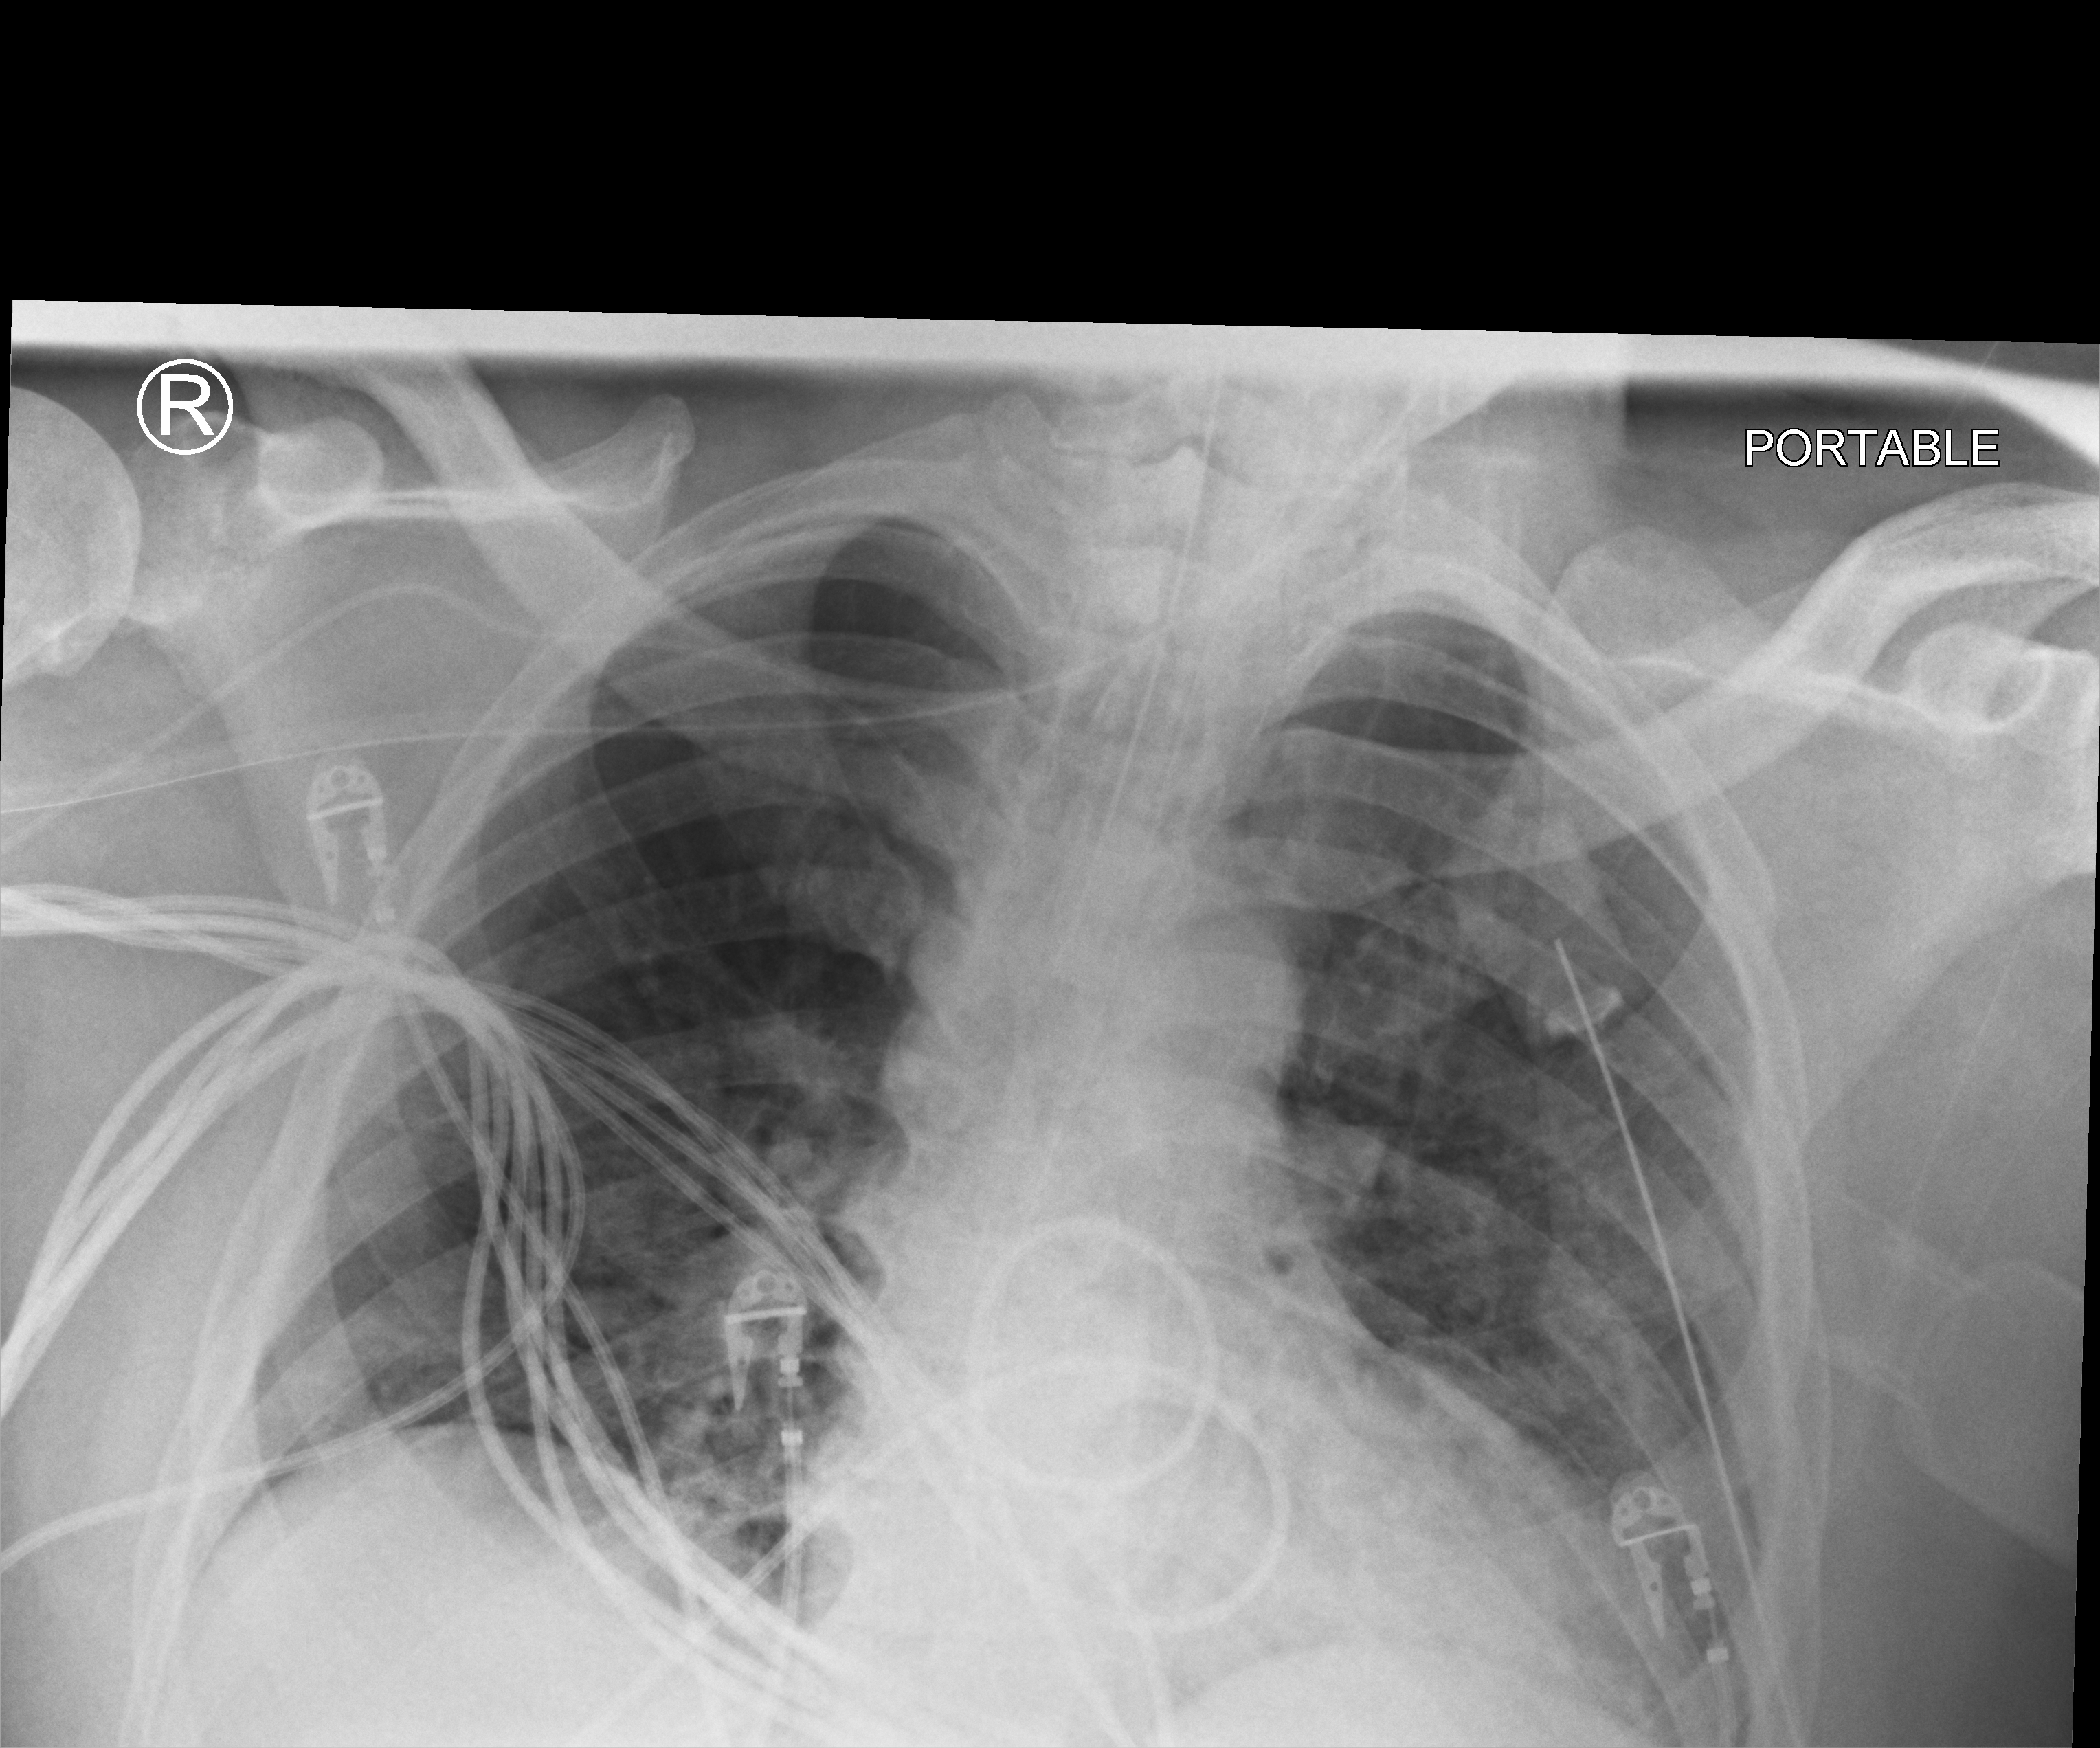
Bedside chest radiograph (computed radiography), anteroposterior (AP) projection. Patient hospitalised with COVID-19; male, aged 18–59 years.
From the hospital-stay record, not from the radiograph (when in the stay this image was taken is not recorded): length of hospital stay: 41 days; admitted to intensive care during this hospital stay: yes; mechanically ventilated during this hospital stay: yes.